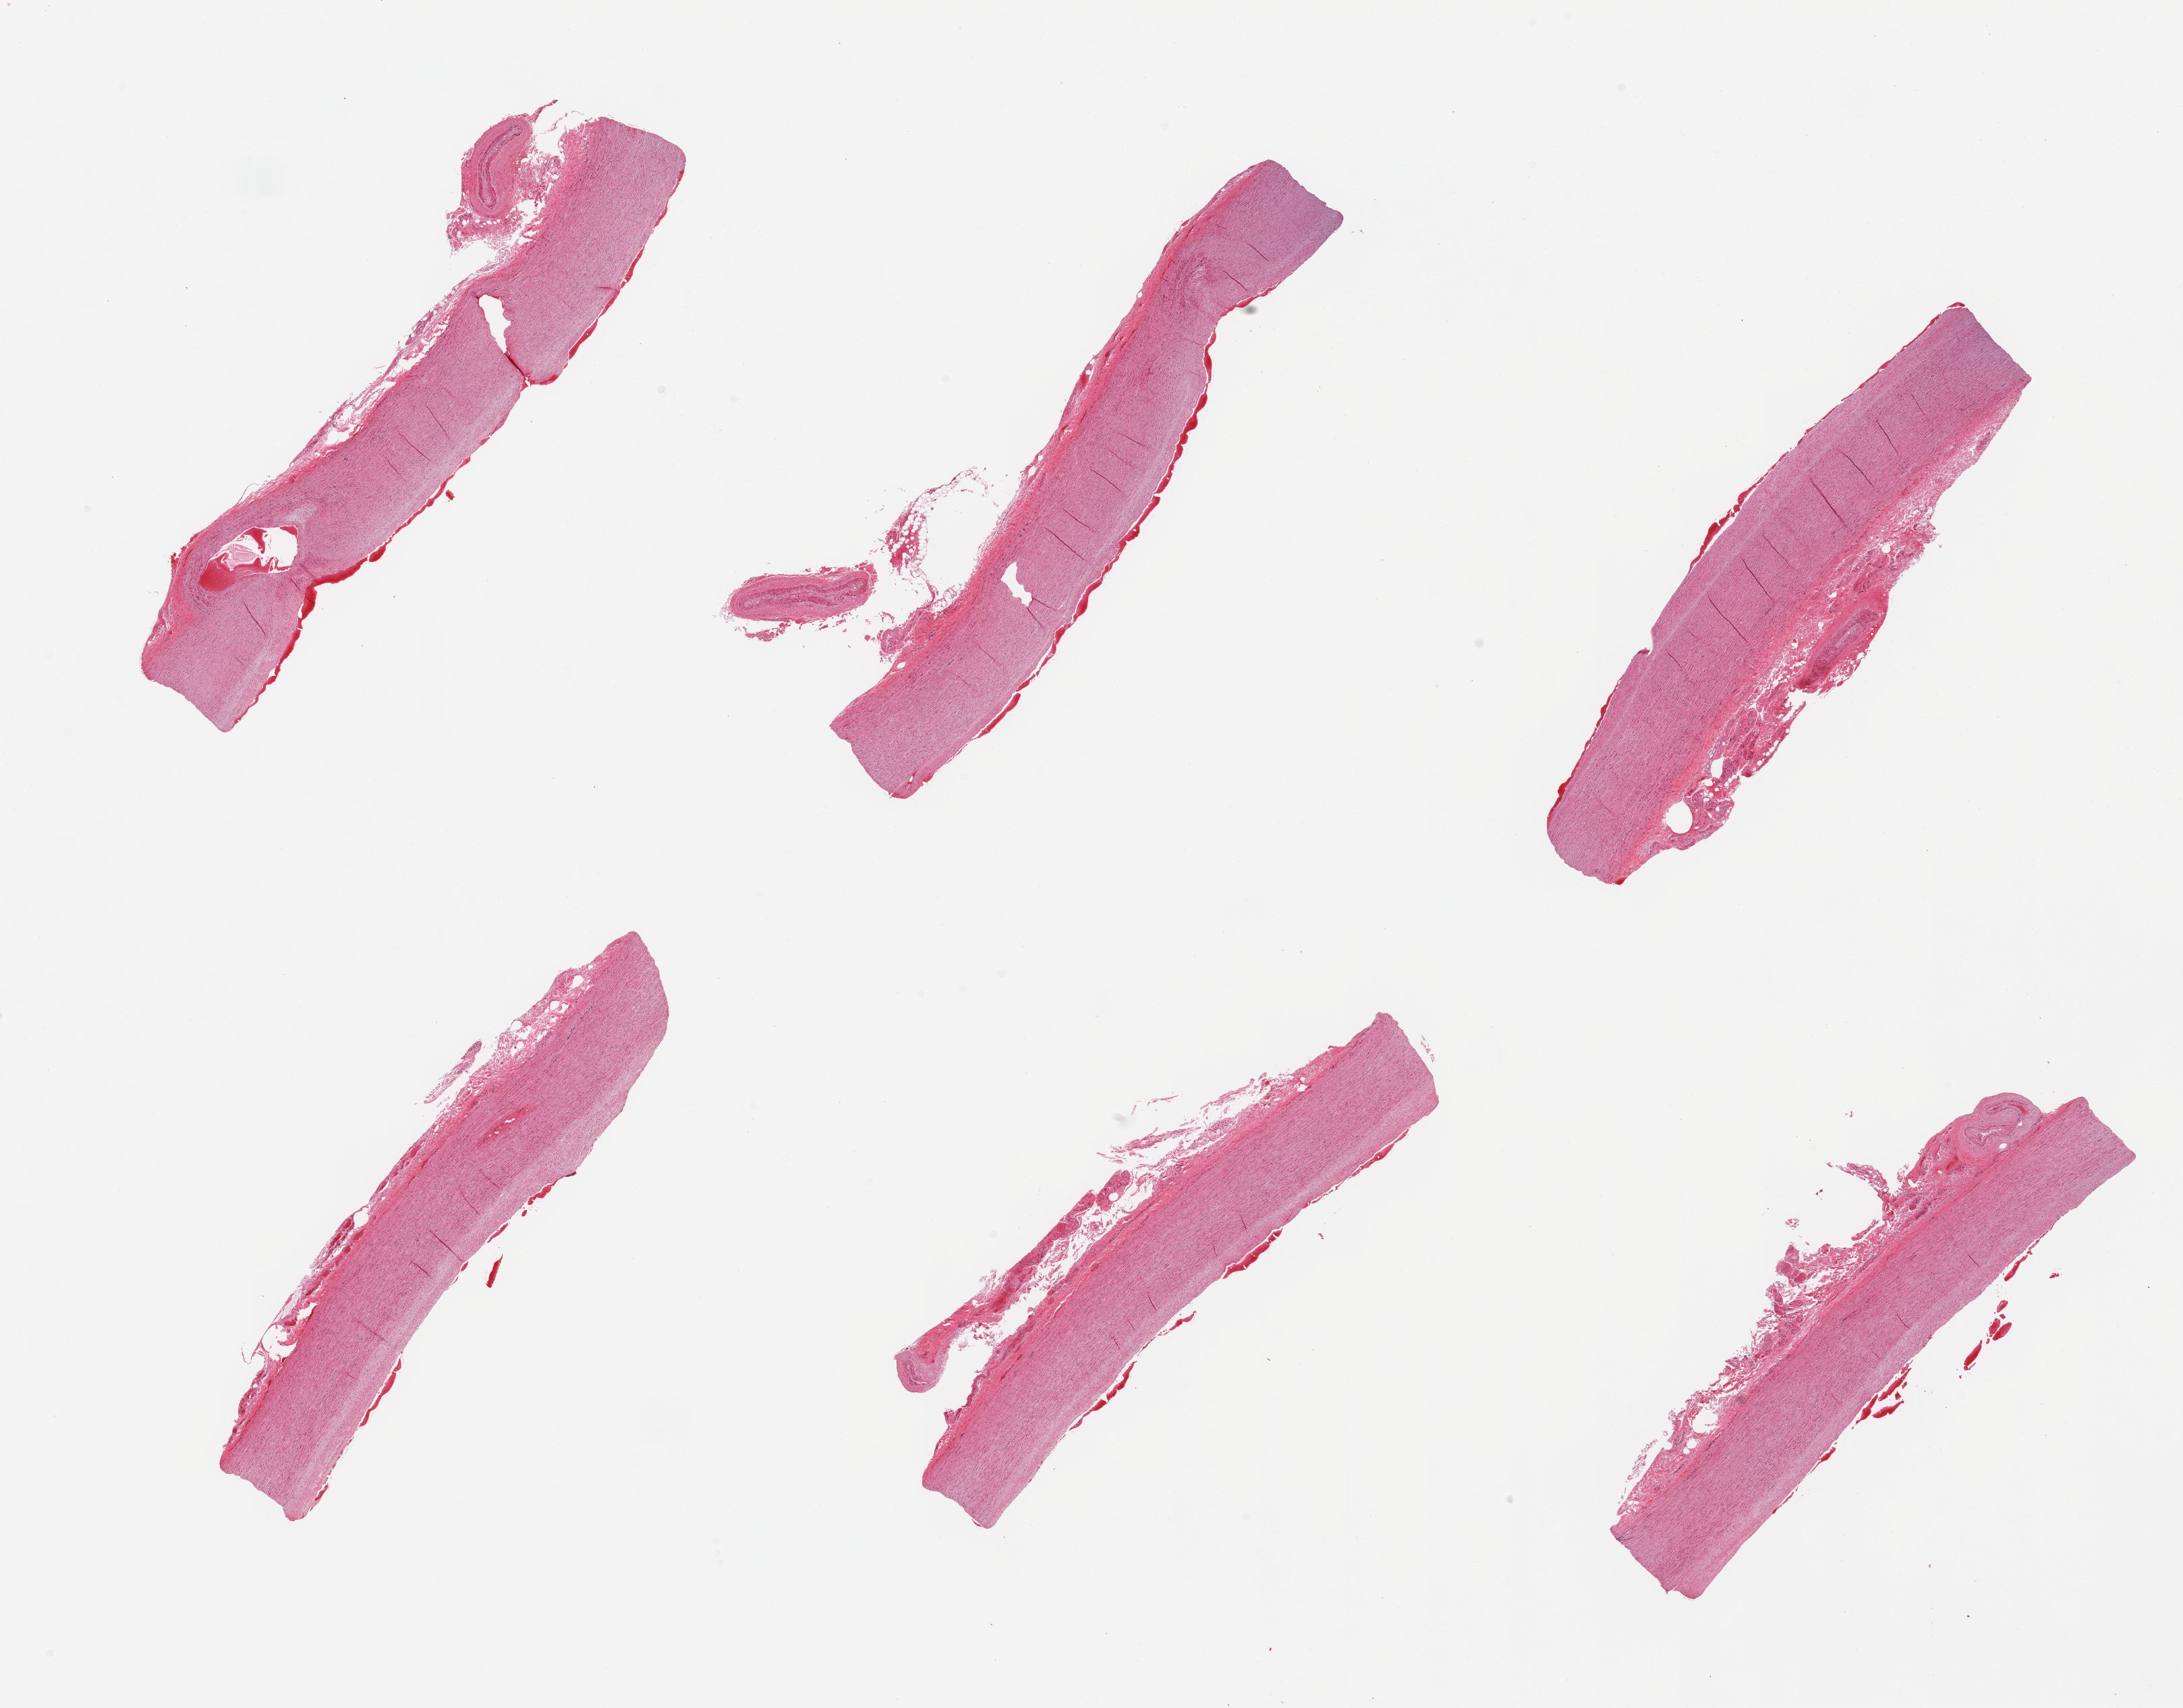
Whole-slide image, H&E stain — low-resolution overview of the scanned area, about 25.6 x 20.0 mm. PAXgene-fixed, paraffin-embedded tissue. Target tissue: aorta. Tissue donor sample. Donor sex: female.
- review note (as recorded): 6 pieces; well trimmed; minimal plaques